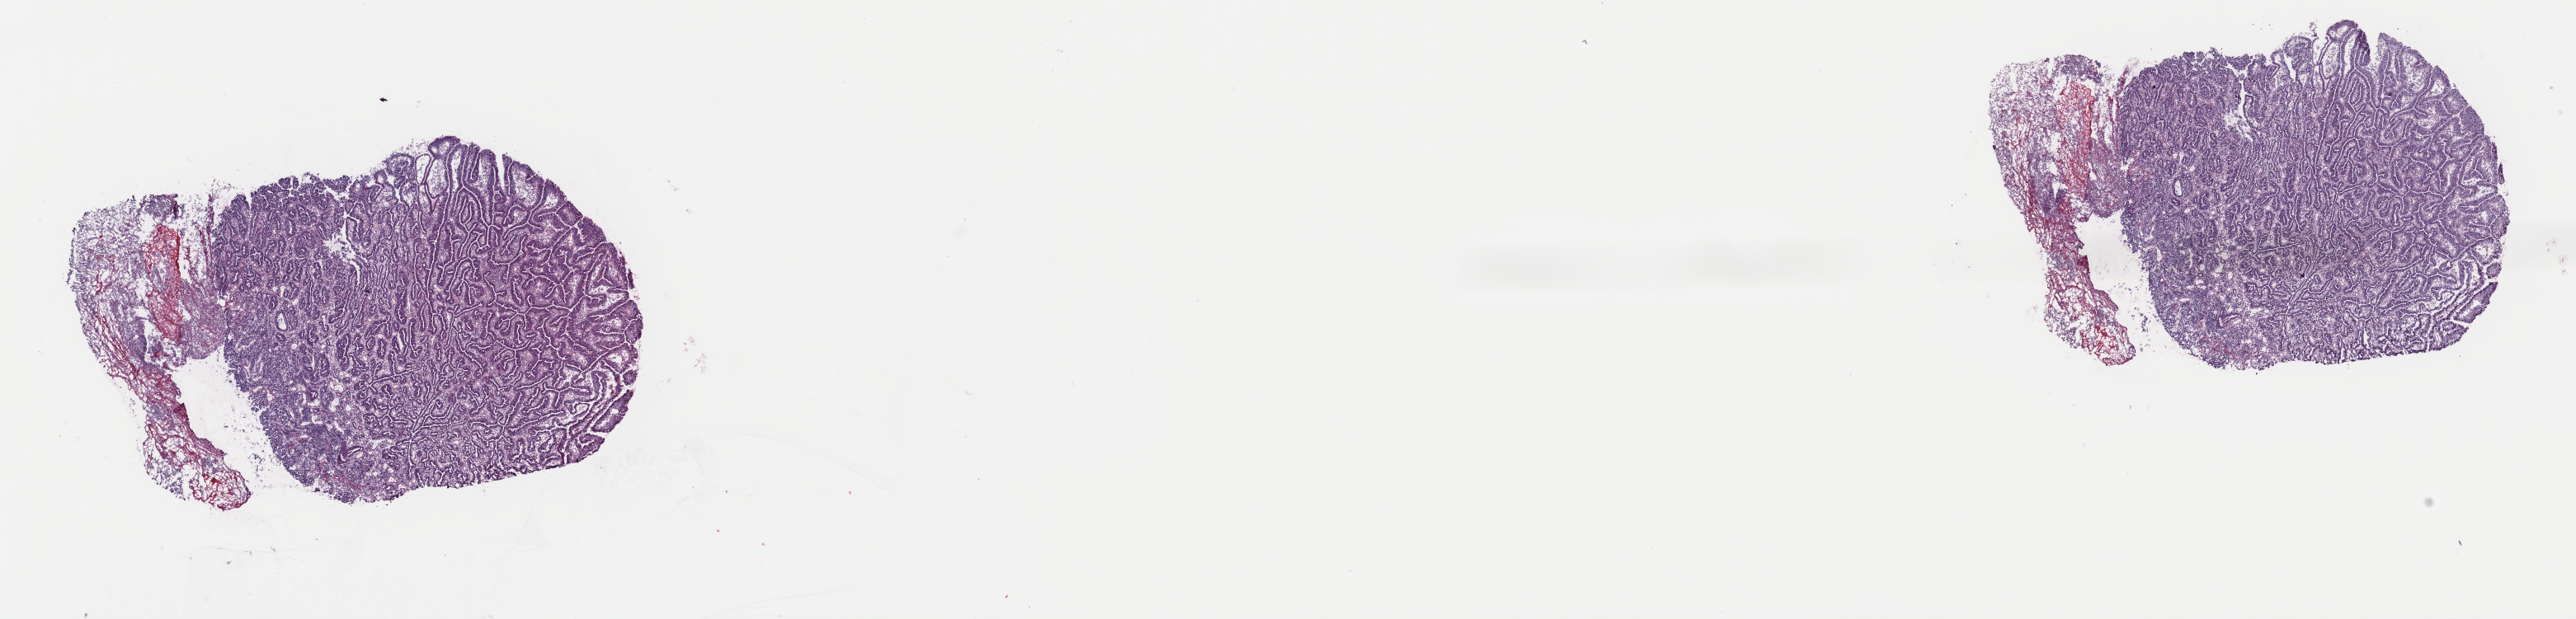
Whole-slide histology image, H&E-stained — whole scanned area (about 24.7 x 5.9 mm, slide scanned at 40x) shown as a low-resolution overview. Frozen section from the top of the tissue portion. Stomach, primary tumour sample. Female, age 71 years at initial diagnosis.
Diagnosis: Adenocarcinoma, NOS (gastric antrum).